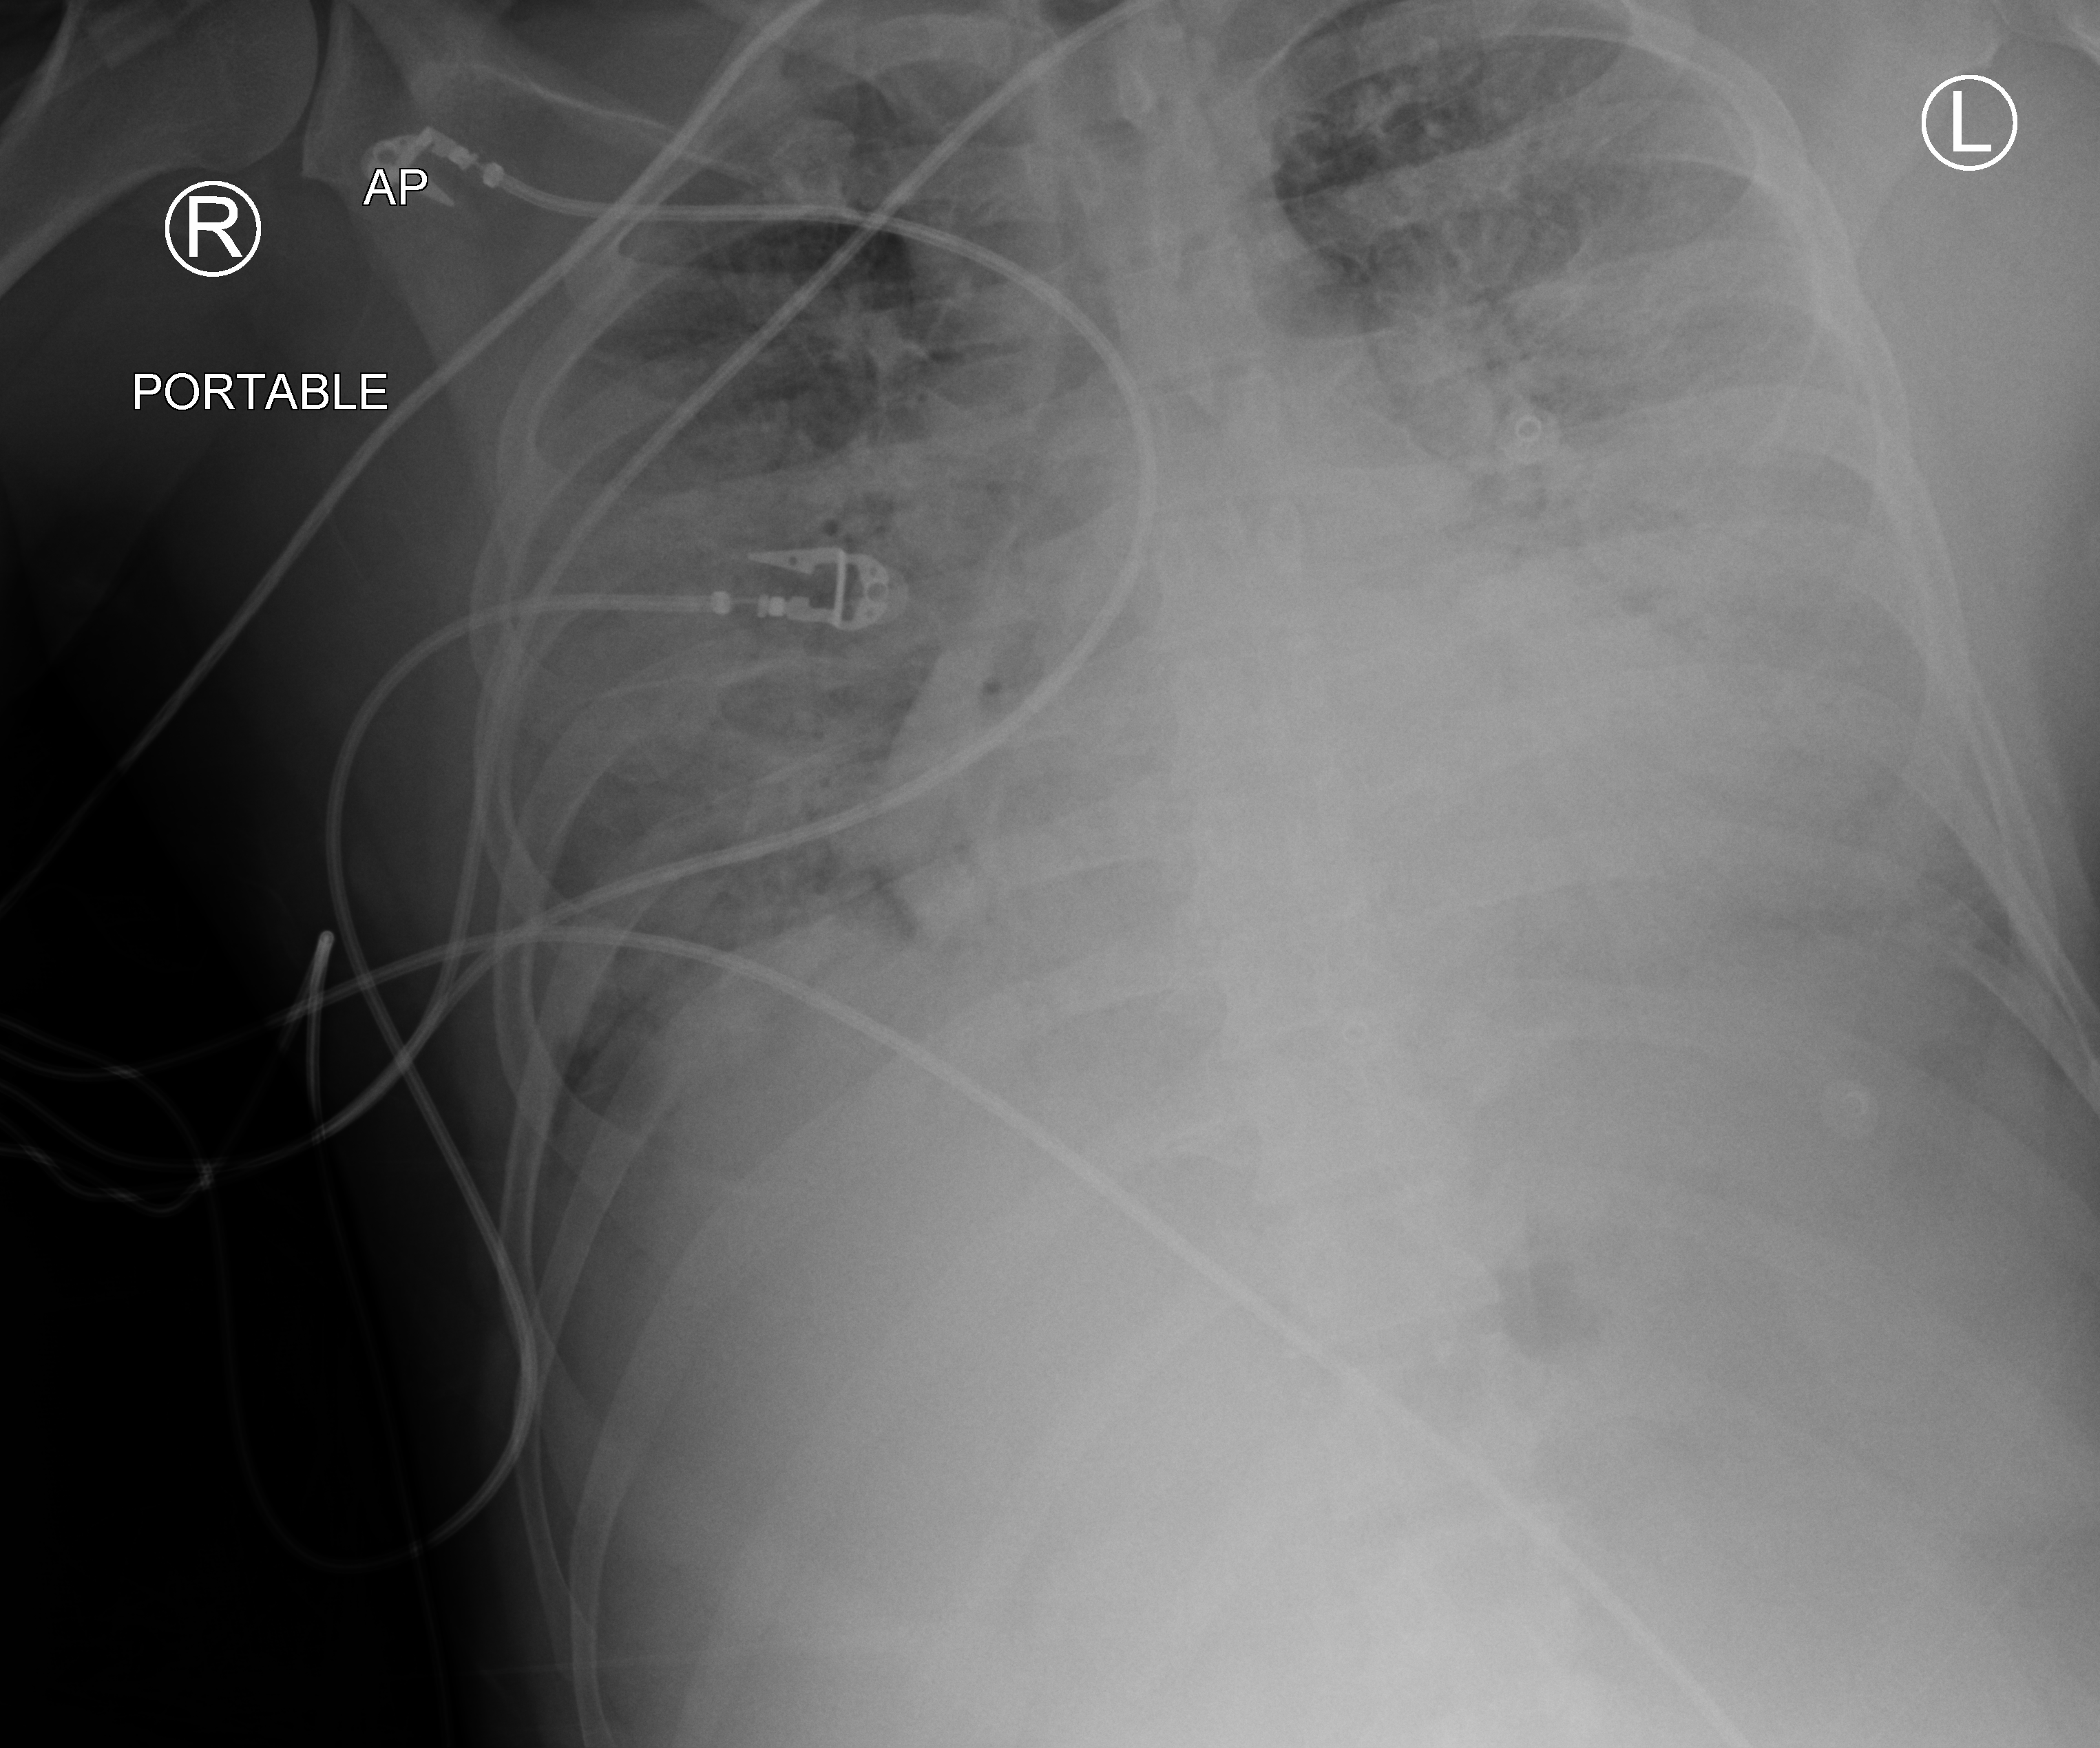
Portable chest radiograph, anteroposterior (AP) projection. Male patient hospitalised with COVID-19, age 18–59 years.
Hospital-stay facts (about this admission, not read from this image; timing relative to this image not recorded): COPD (admission record): no; other chronic lung disease (admission record): no.